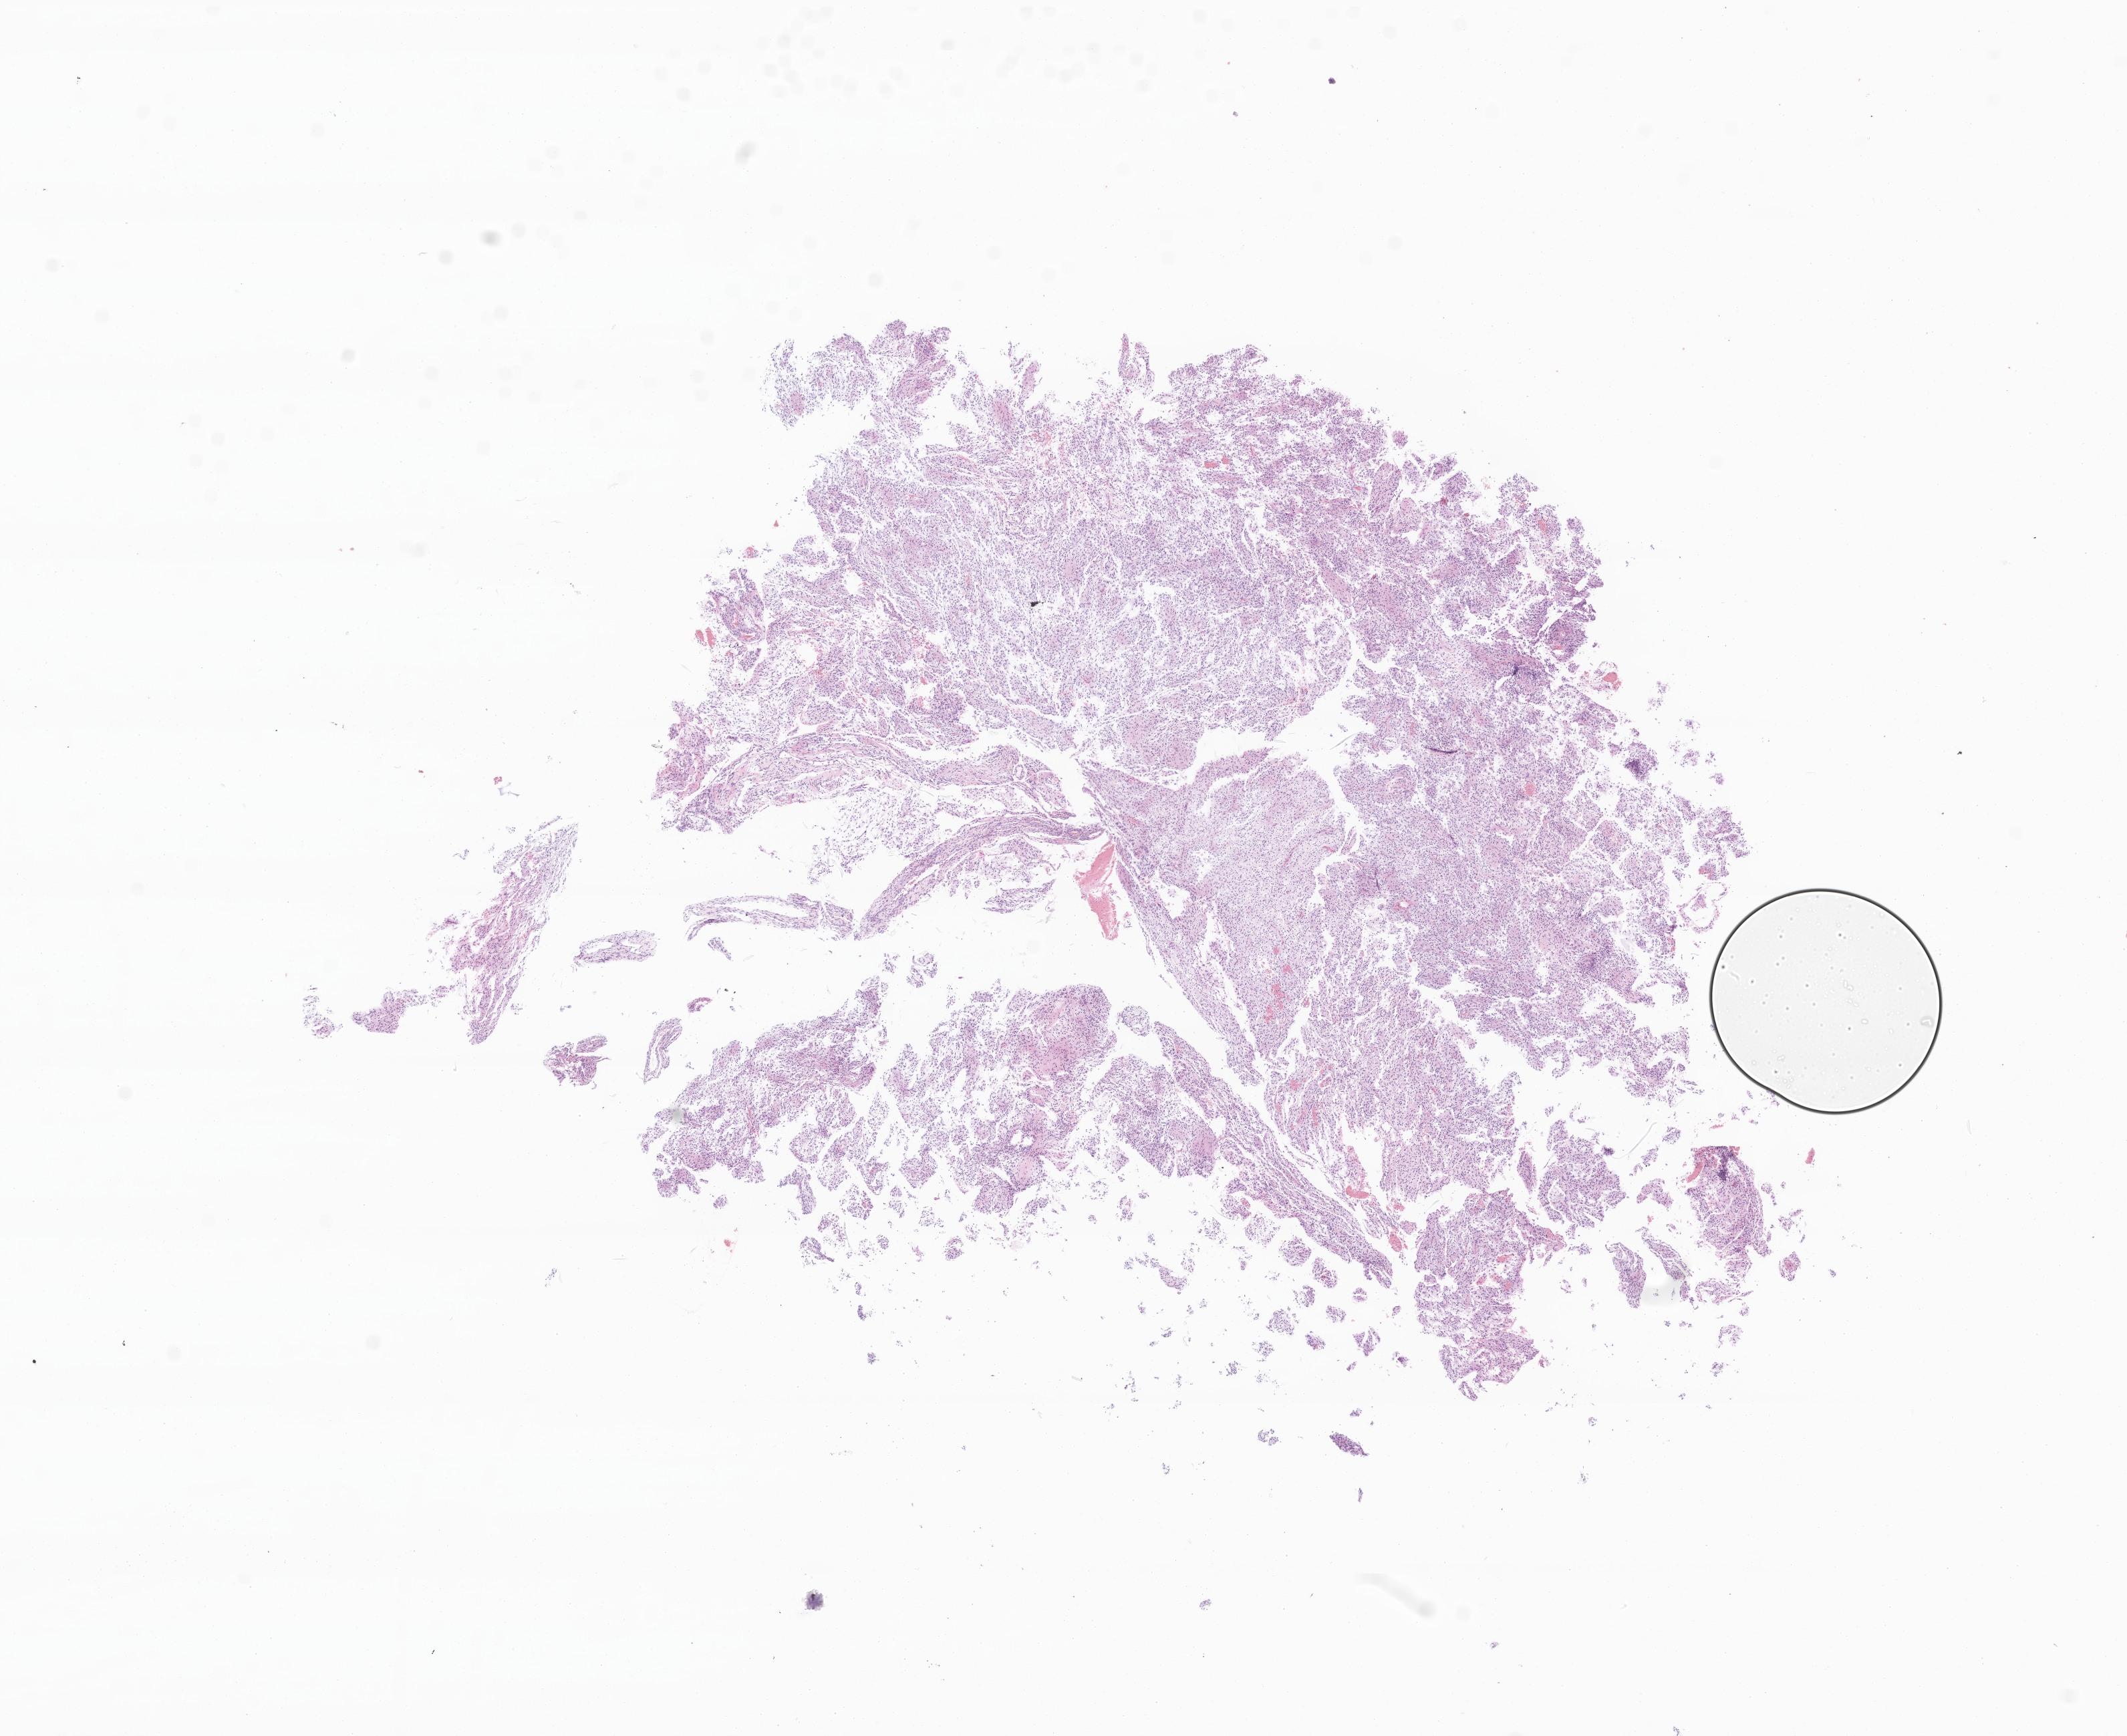
H&E whole-slide image of tumor tissue from the brain — low-resolution overview of the scanned area, about 13.4 x 11.0 mm; formalin-fixed, paraffin-embedded (FFPE) tissue. Patient: male, age 50 months (4 years 2 months).
• diagnosis (ICD-O-3 morphology term): Glioma, malignant